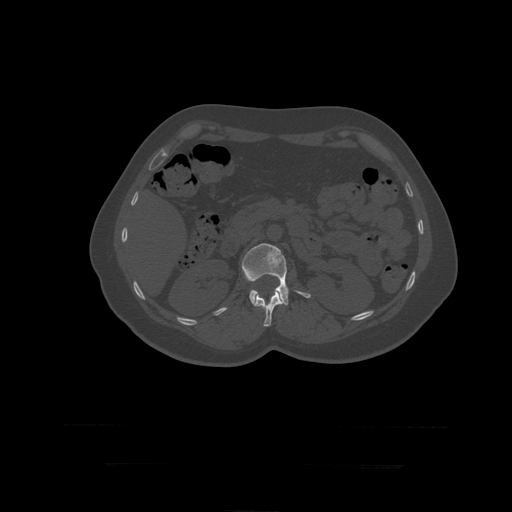
CT including the spine, one axial slice; position 160 of 399 along the scan axis; reconstruction kernel STANDARD; 120 kVp; bone window (W 1800 / L 400 HU); 512 × 512 image matrix, field of view 450 × 450 mm. Patient age 41 years. From the clinical record (not read from this slice): primary cancer: breast.
Structures marked on this image (semi-automatic segmentation, software-assisted and operator-edited):
- L1 vertebra: bounding box (x1, y1, x2, y2) in pixels: (254, 291, 284, 327)
- L2 vertebra: (242, 244, 311, 305)